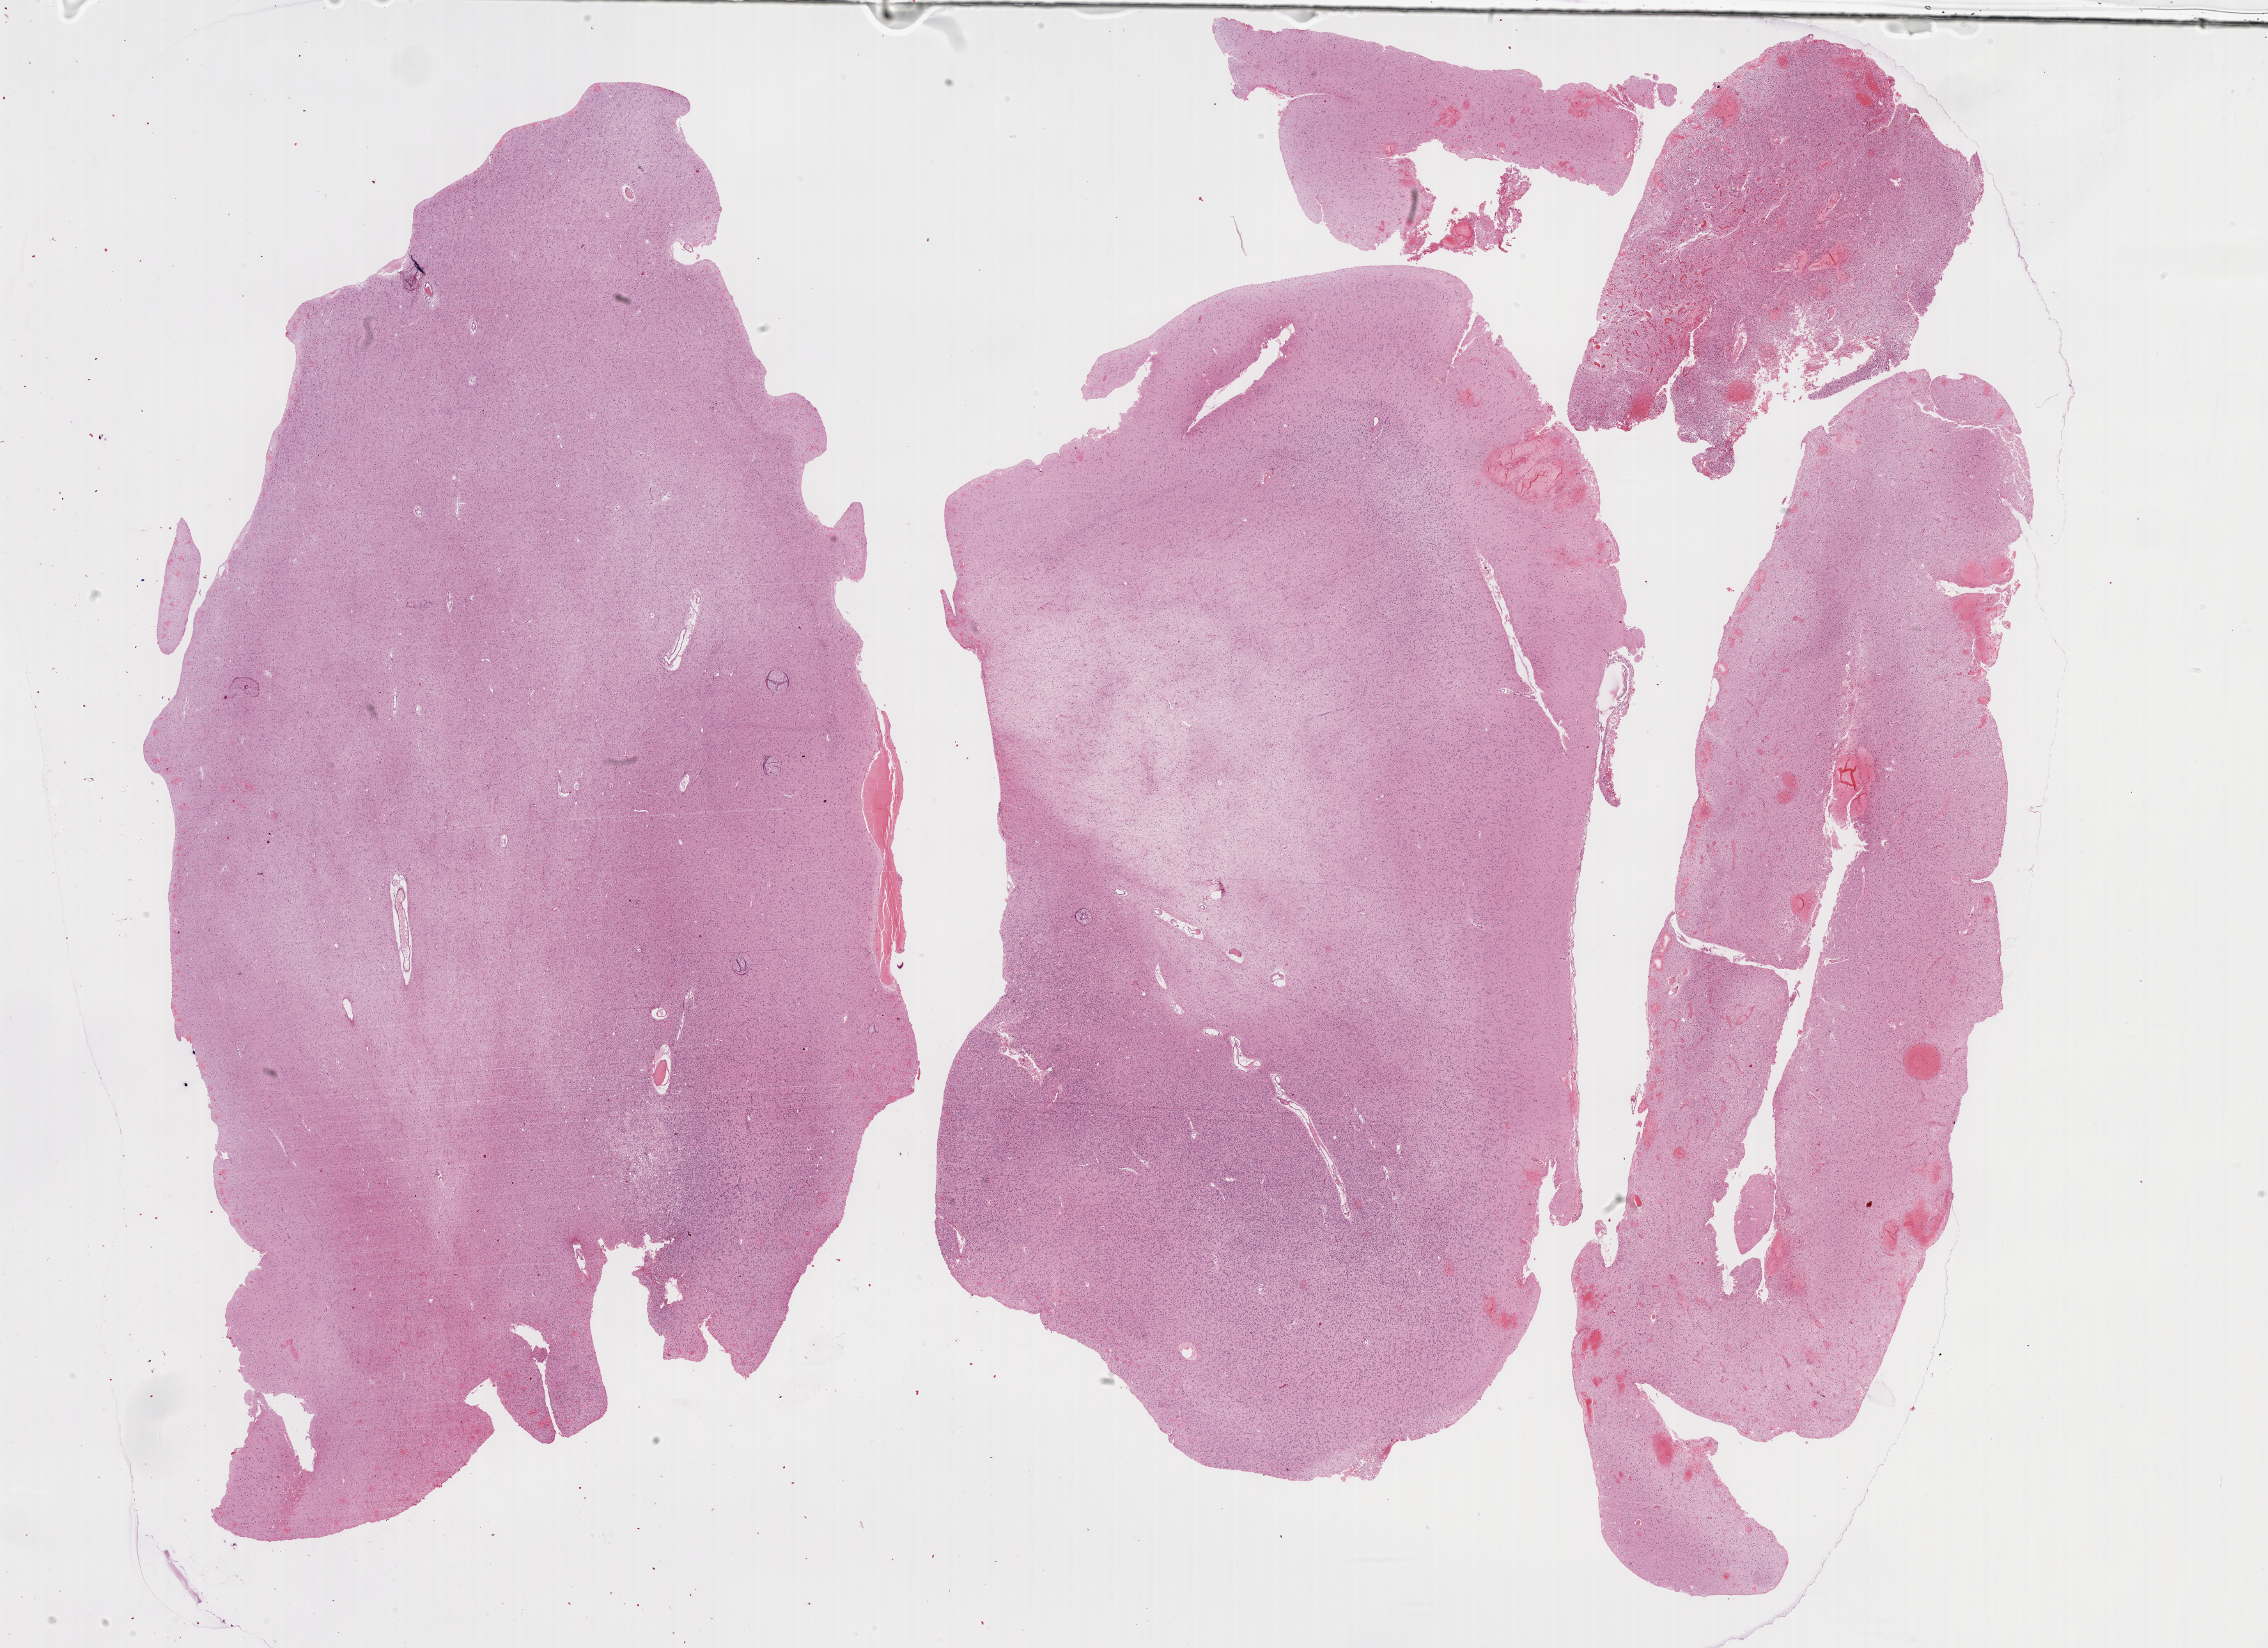
Whole-slide histology image, Hematoxylin and eosin (H&E) stained — whole scanned area (about 28.7 x 20.8 mm) shown as a low-resolution overview; formalin-fixed paraffin-embedded (FFPE) diagnostic section; brain, primary tumour sample. Male, age 33 years at initial diagnosis. Histologic grade: G2 (moderately differentiated).
Laterality: left. Pathologic diagnosis: Oligodendroglioma, NOS (cerebrum).